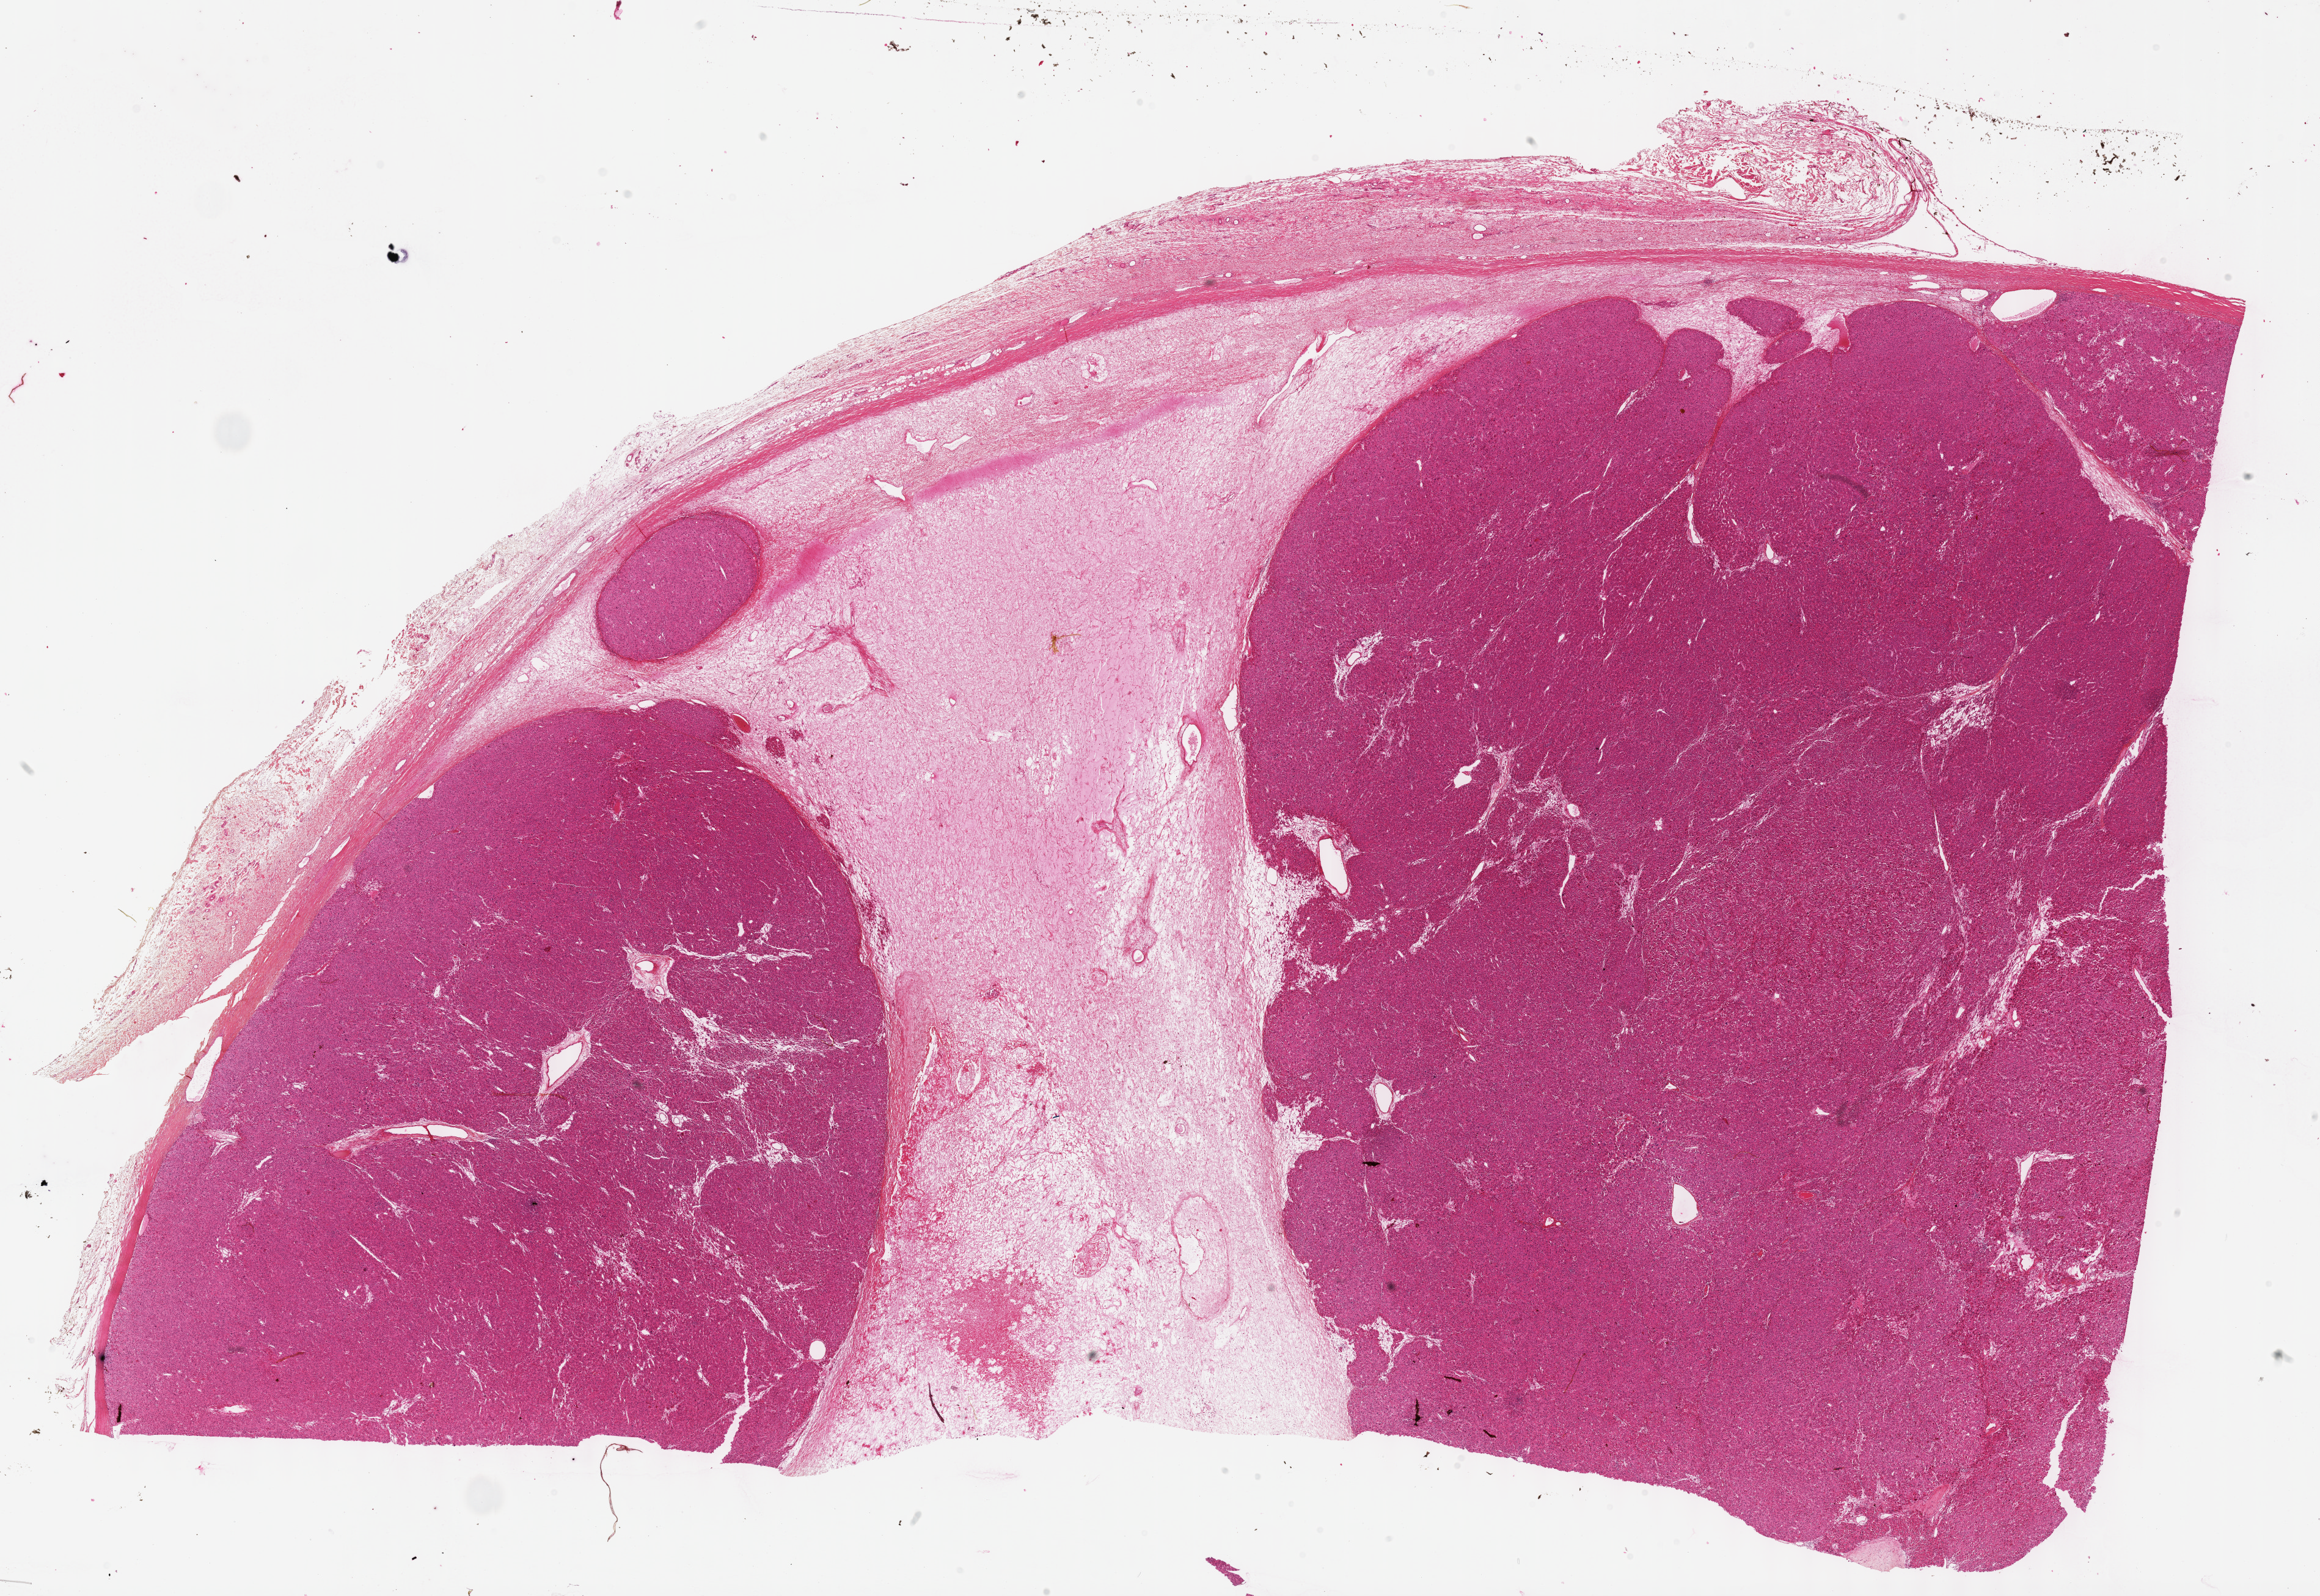
Whole-slide histology image, H&E-stained, shown as a low-resolution overview of the whole scanned area (about 30.7 x 21.1 mm), formalin-fixed paraffin-embedded (FFPE) diagnostic section, primary tumour sample from the adrenal cortex. Female, age 31 years at initial diagnosis.
* laterality: right
* diagnosis: Adrenal cortical carcinoma